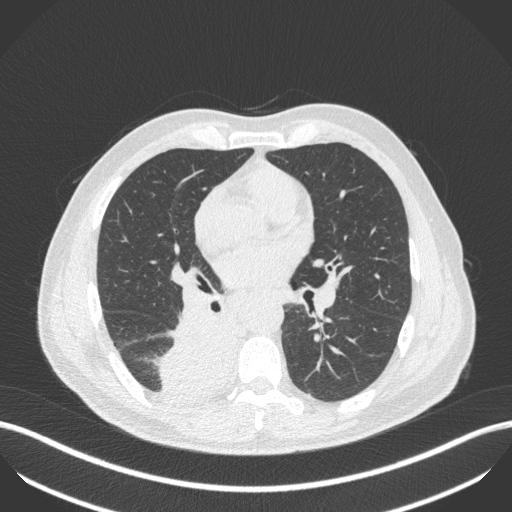
Chest CT, one axial slice. Slice 246 of 451 in the series (ordered by position). Lung window (W 1500 / L -600 HU). 1 mm slice thickness. 512 × 512 image matrix, field of view 400 × 400 mm. Male patient, age 61 years. From the clinical record (not read from this slice): clinical TNM (as recorded): T1 N0 M0.
Structures marked on this image (rectangle marked by the reading radiologist):
- lung tumour (recorded histology: small cell carcinoma): box from (x=153, y=302) to (x=239, y=402) px